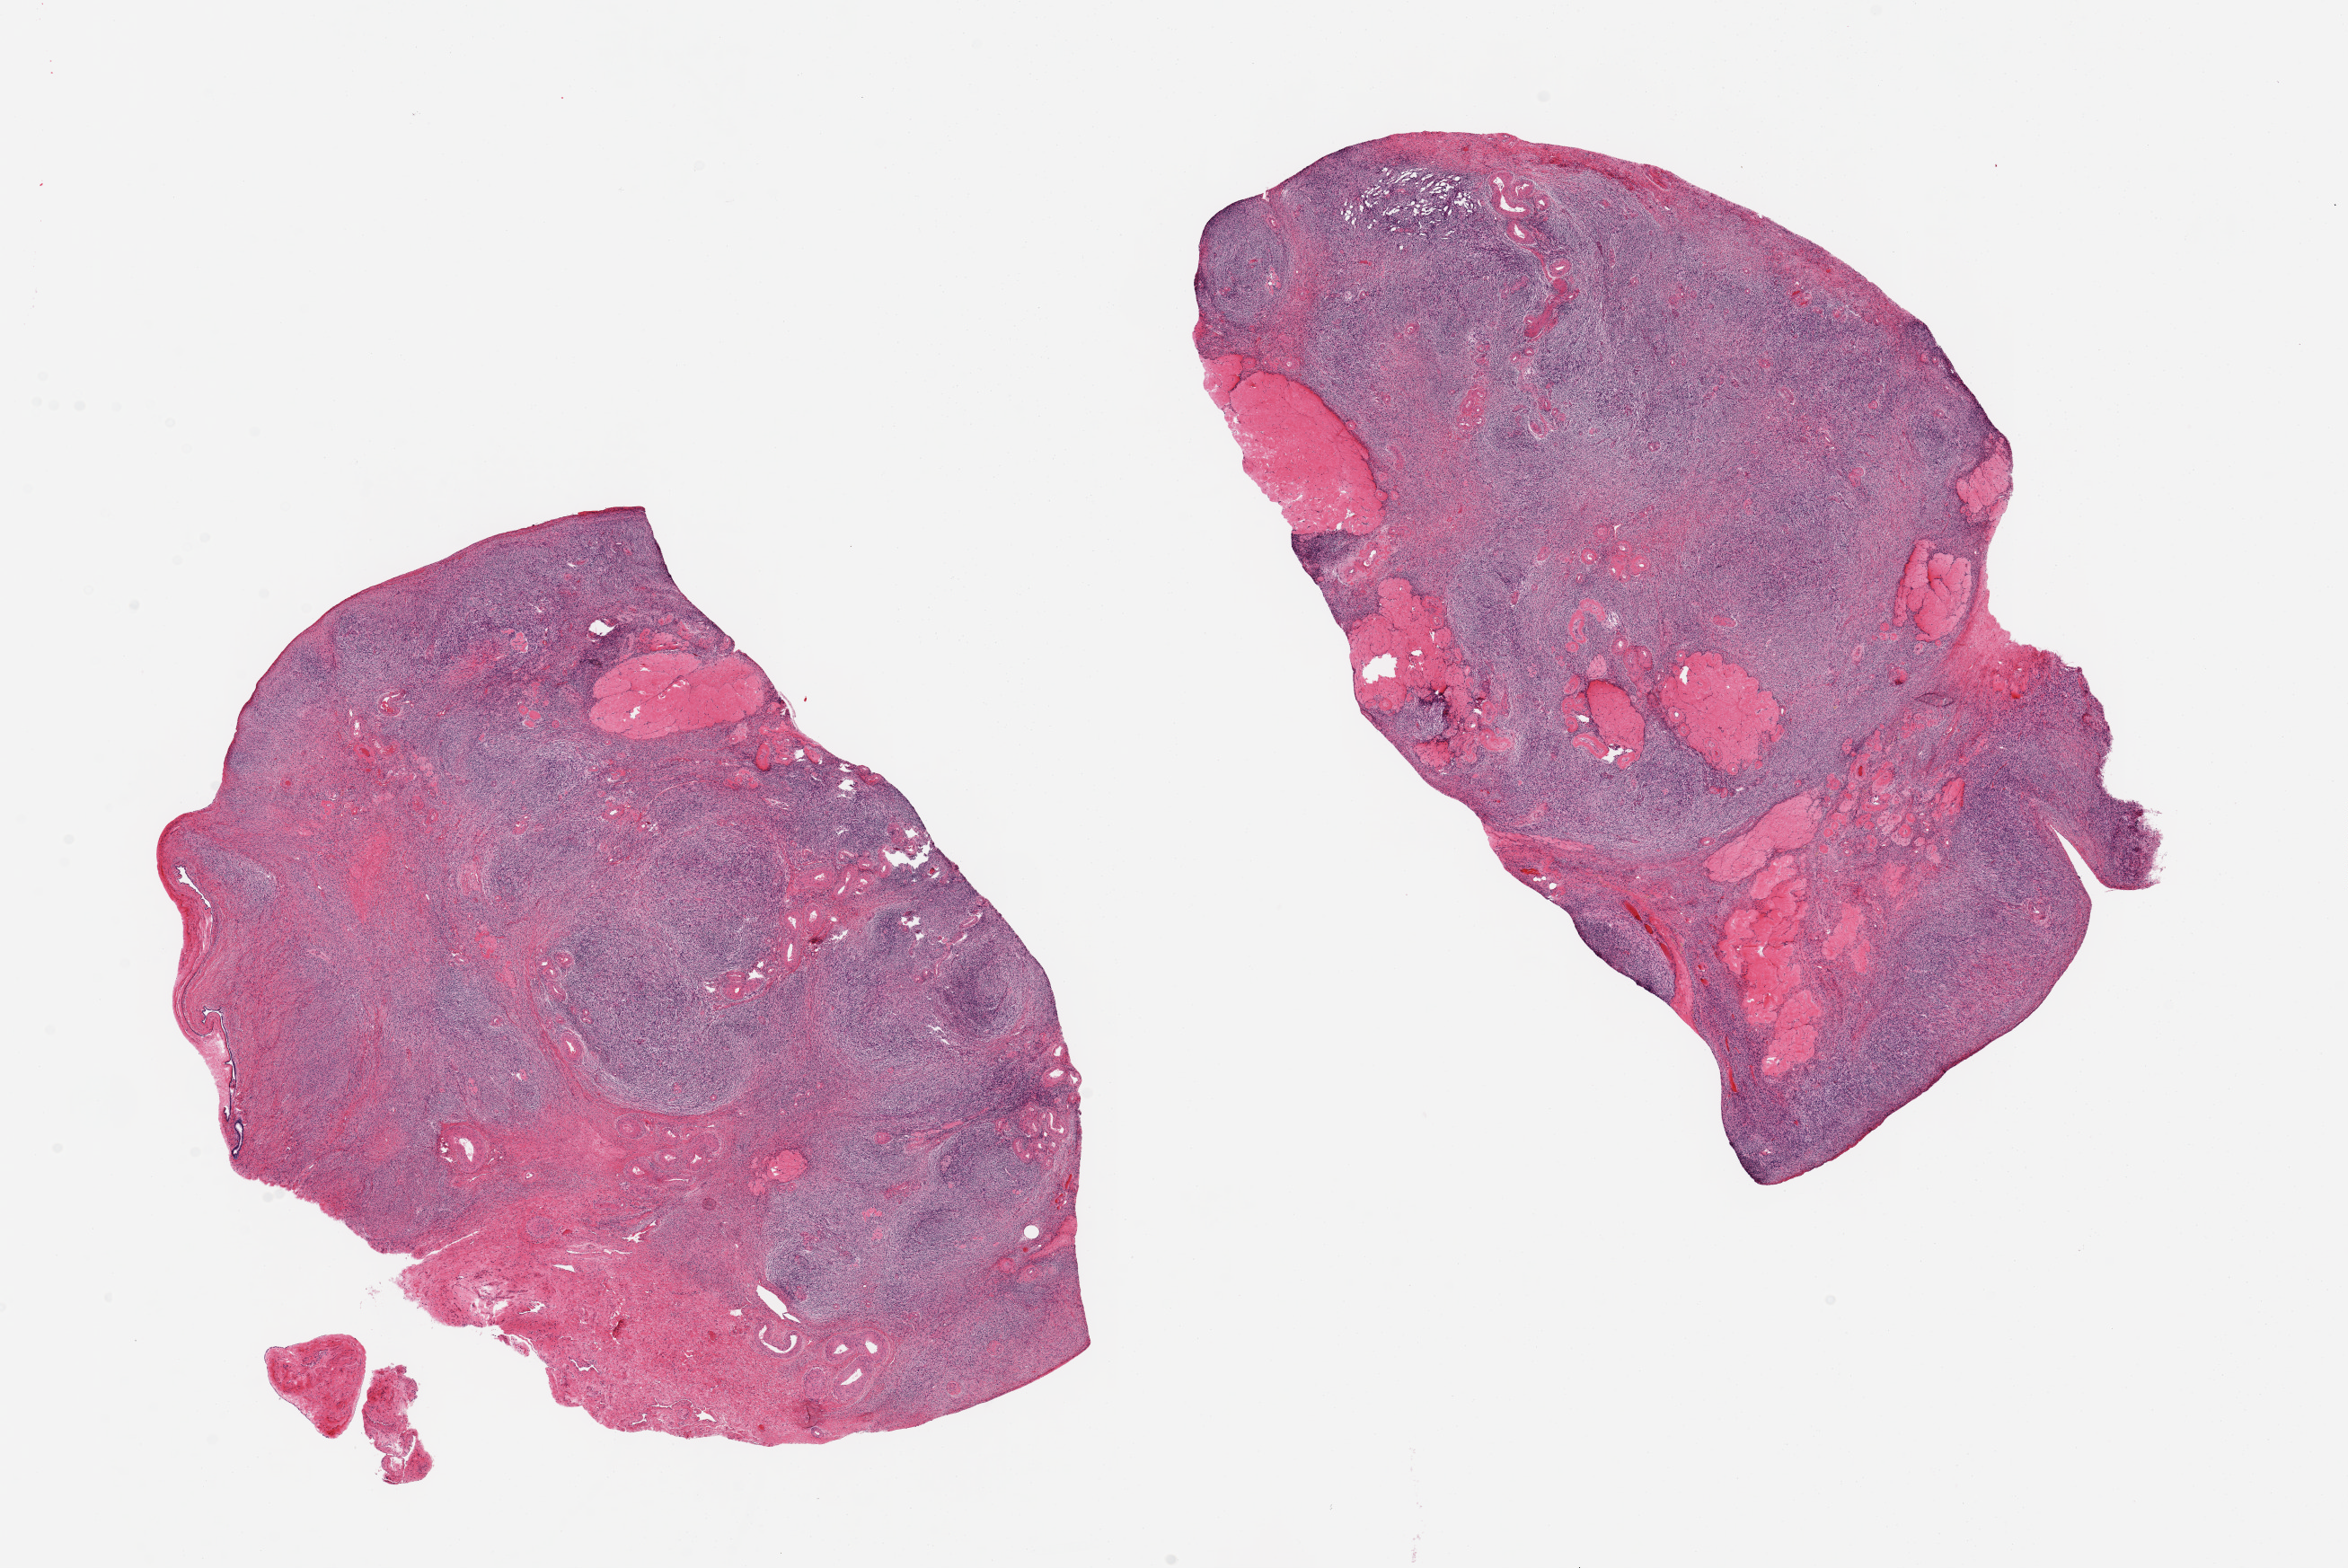
Hematoxylin and eosin (H&E) whole-slide image, brightfield, a low-resolution overview of the entire scanned area, about 20.7 x 13.8 mm, PAXgene-fixed, paraffin-embedded tissue, target tissue: ovary, tissue donor sample. Donor: female.
Review note (as recorded): 2 aliquots, ~9x7mm. Postmenopausal atrophy, prominent corpora albicantia.